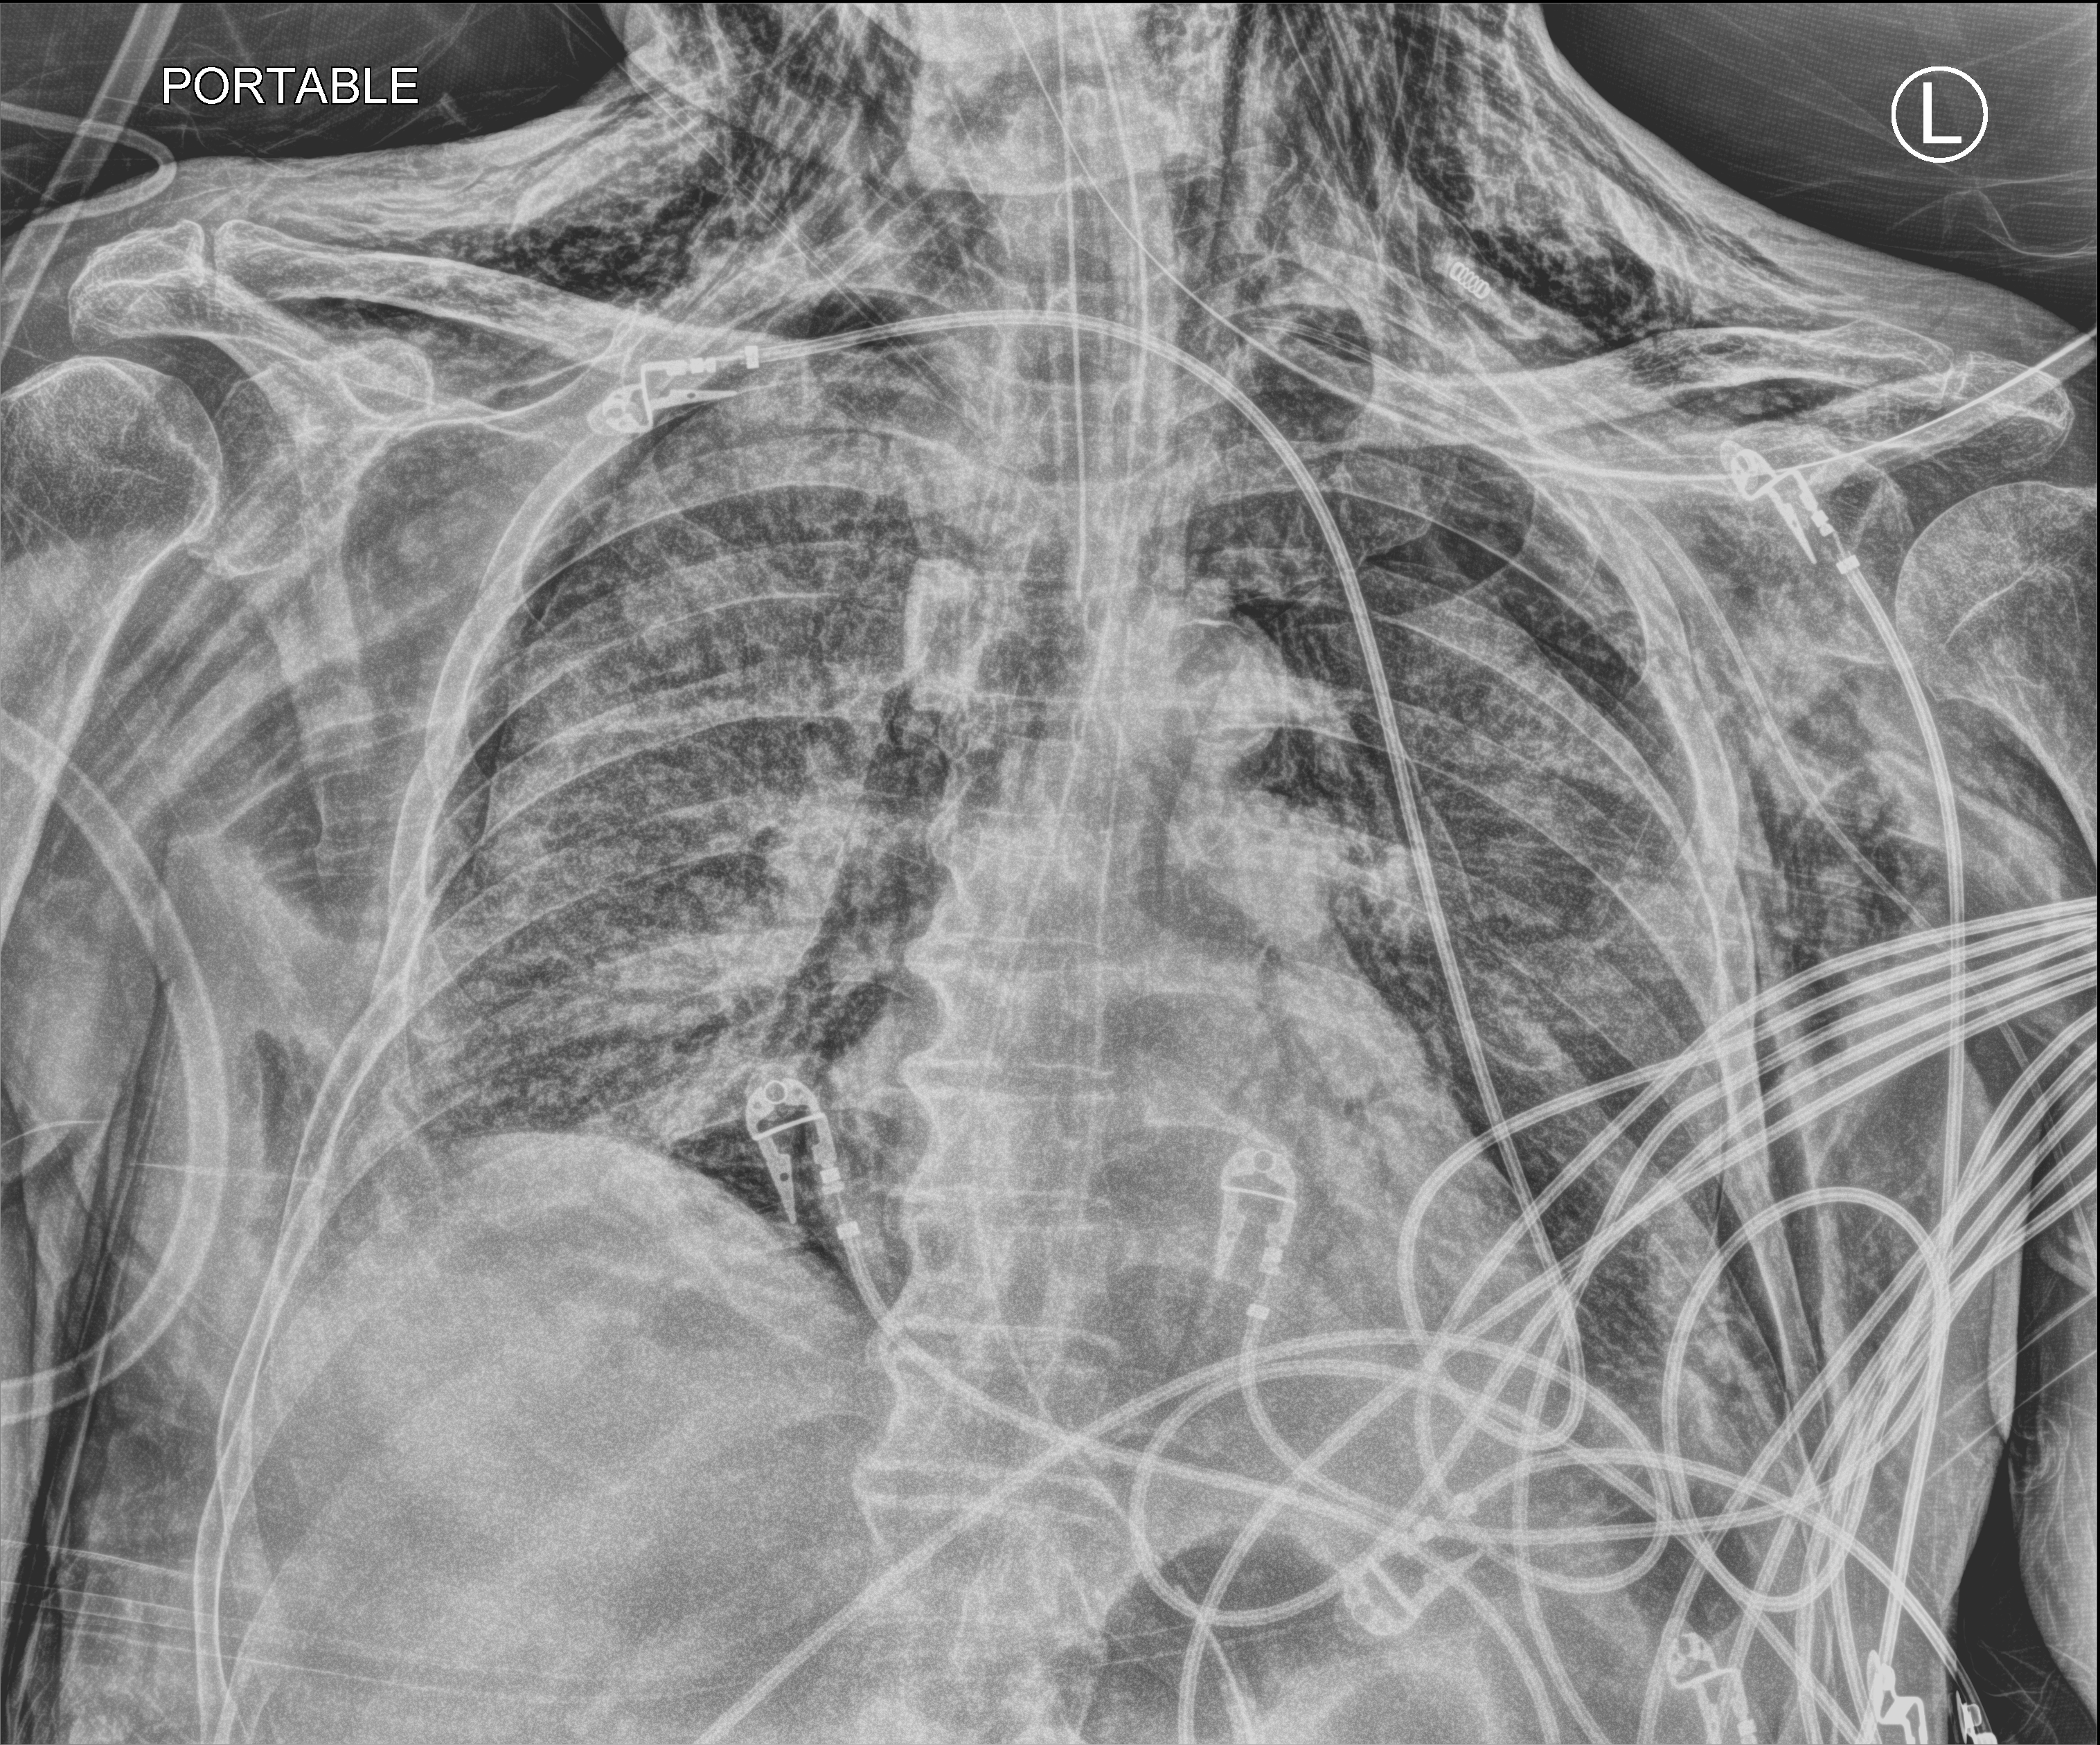
Bedside chest radiograph (computed radiography); anteroposterior (AP) projection. Male patient hospitalised with COVID-19, age 75–90 years.
Hospital-stay facts (about this admission, not read from this image; timing relative to this image not recorded): length of hospital stay: 30 days; mechanically ventilated during this hospital stay: yes; admitted to intensive care during this hospital stay: yes.